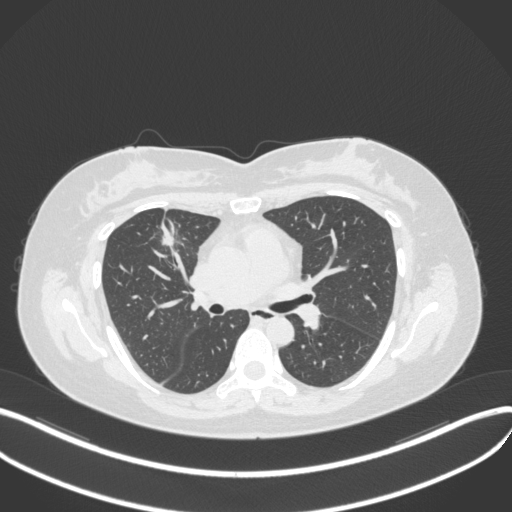
Chest CT, one axial slice. Slice 187 of 272 in the series (ordered by position). Reconstruction kernel B31f. Lung window (W 1500 / L -600 HU). 1 mm slice thickness. 512 × 512 image matrix, field of view 400 × 400 mm. Female patient, age 42 years. Case-level facts recorded for this patient, not image findings: clinical TNM (as recorded): T1b N0 M0.
Structures marked on this image (bounding box drawn by a radiologist):
- lung tumour (recorded histology: adenocarcinoma): bounding box [x1, y1, x2, y2] px = [155, 218, 185, 249]